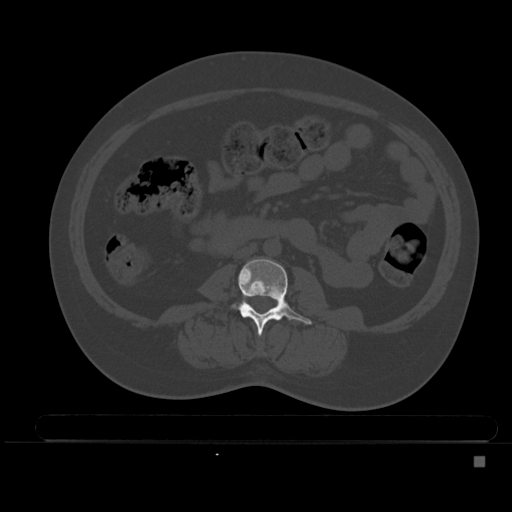
CT including the spine, one axial slice; position 150 of 495 along the scan axis; bone window (W 1800 / L 400 HU); 1.5 mm slice thickness; 512 × 512 image matrix, field of view 404 × 404 mm. Patient: female, 33 years. From the clinical record (not read from this slice): primary cancer: breast.
Structures marked on this image (semi-automatic segmentation, software-assisted and operator-edited):
- L3 vertebra: bounding box <231,259,312,335> (left, top, right, bottom; pixels)